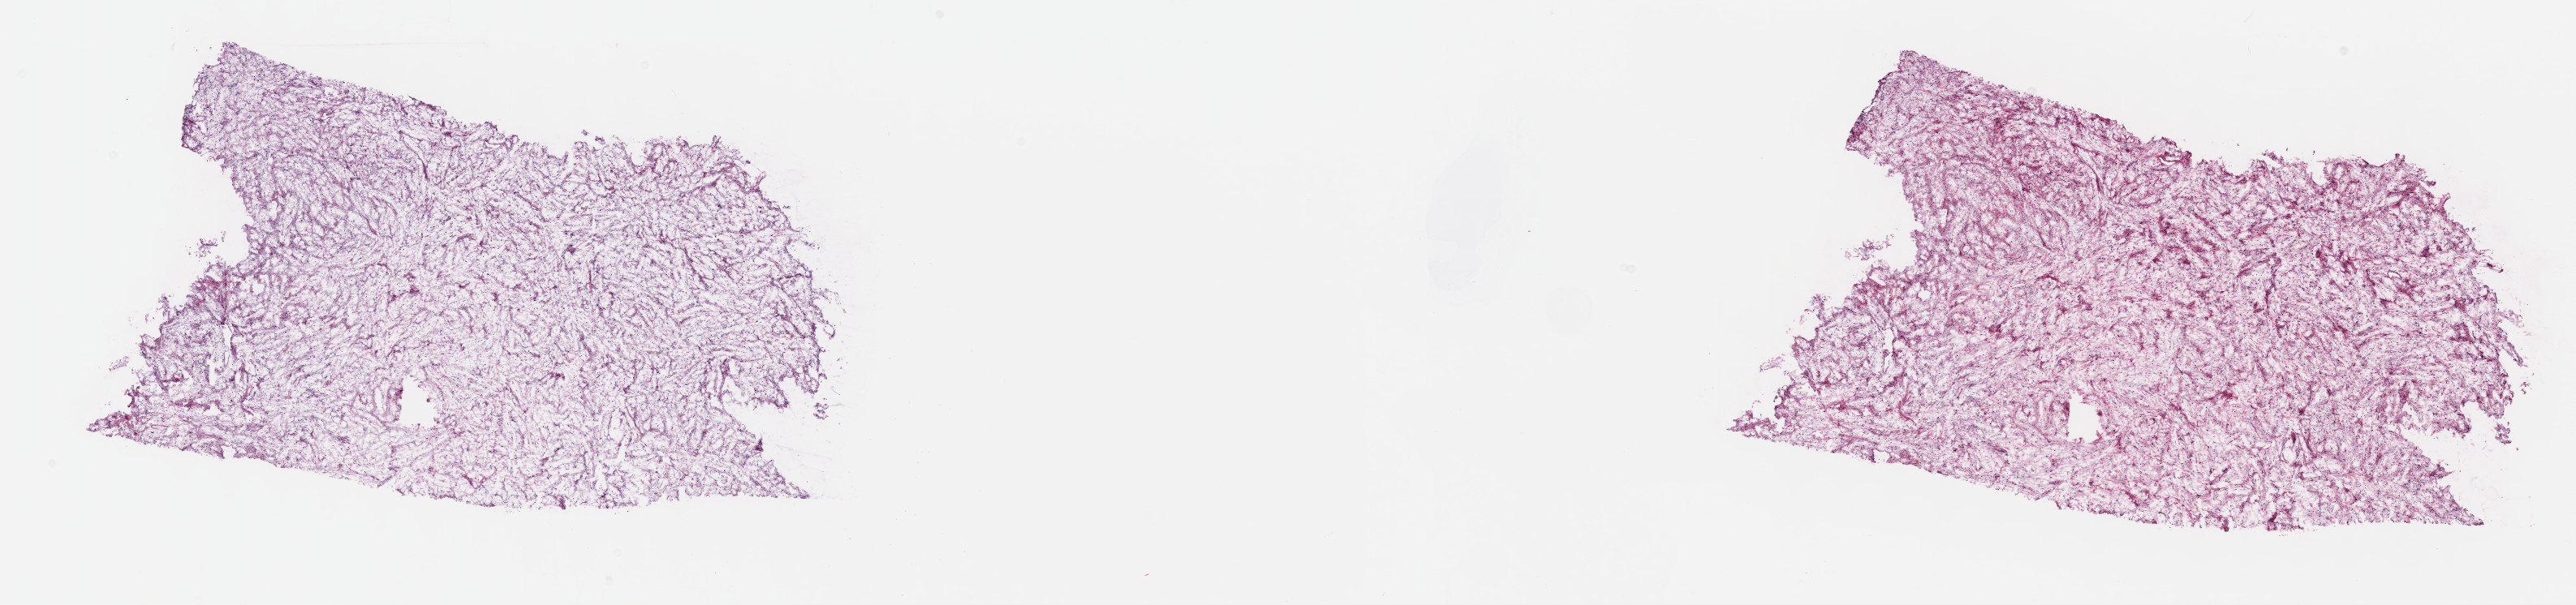
Digitized Hematoxylin and eosin (H&E) stained tissue section (whole slide) — low-resolution overview of the scanned area, about 25.7 x 6.0 mm (acquisition: 40x scan). Frozen section from the top of the tissue portion. Sample: primary tumour, connective, subcutaneous and other soft tissues. Male patient; age at initial diagnosis 75 years. Pathologist review of this section (percent, as recorded): tumour cells 90%, tumour nuclei 95%, normal cells 0%, stromal cells 10%, necrosis 0%. Infiltration values recorded for this section: lymphocyte infiltration 0%, monocyte infiltration 0%, neutrophil infiltration 0%.
* histologic diagnosis: Fibromyxosarcoma (connective, subcutaneous and other soft tissues of thorax)